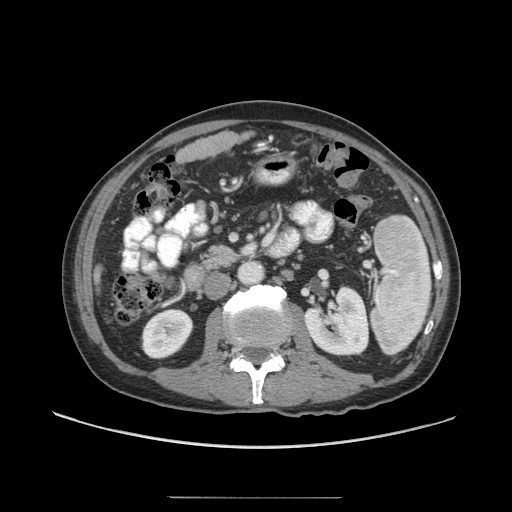
Contrast-enhanced abdominal CT (liver protocol), one axial slice. Position 11 of 71 along the scan axis. Reconstruction kernel STANDARD. Soft-tissue window (W 400 / L 40 HU). 512 × 512 image matrix, field of view 400 × 400 mm. From the clinical record (not read from this slice): diagnosis: hepatocellular carcinoma (patient treated with transarterial chemoembolisation; whether this scan precedes or follows treatment is not stated here); TNM stage (as recorded): Stage-I; Child-Pugh class: A; tumour differentiation: well differentiated; tumour nodularity: uninodular.
Annotated regions visible in this slice (semi-automatically segmented with operator editing):
- liver parenchyma outside the tumour (the mass and vessels are separate outlines, so this box may not span the whole liver): bounding box (x1, y1, x2, y2) in pixels: (94, 148, 188, 290)